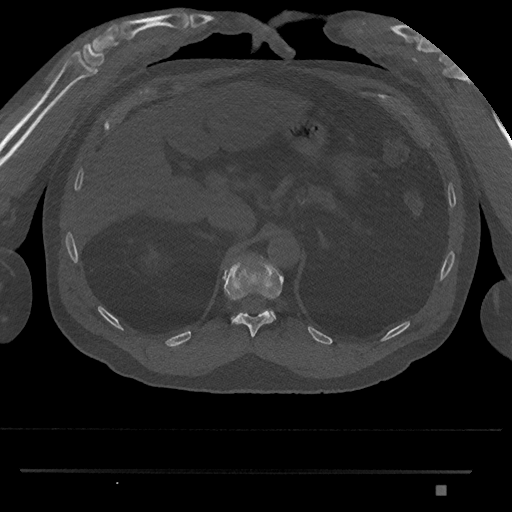
CT including the spine, one axial slice; reconstruction kernel Br40s/3; 120 kVp; bone window (W 1800 / L 400 HU); 0.5 mm slice thickness; 512 × 512 image matrix, field of view 429 × 429 mm. Male patient, age 65 years. Case-level facts recorded for this patient, not image findings: primary cancer: prostate.
Structures marked on this image (semi-automatic segmentation, software-assisted and operator-edited):
- T11 vertebra: bounding box [x1, y1, x2, y2] px = [222, 260, 284, 338]
- T12 vertebra: [231, 310, 276, 319]